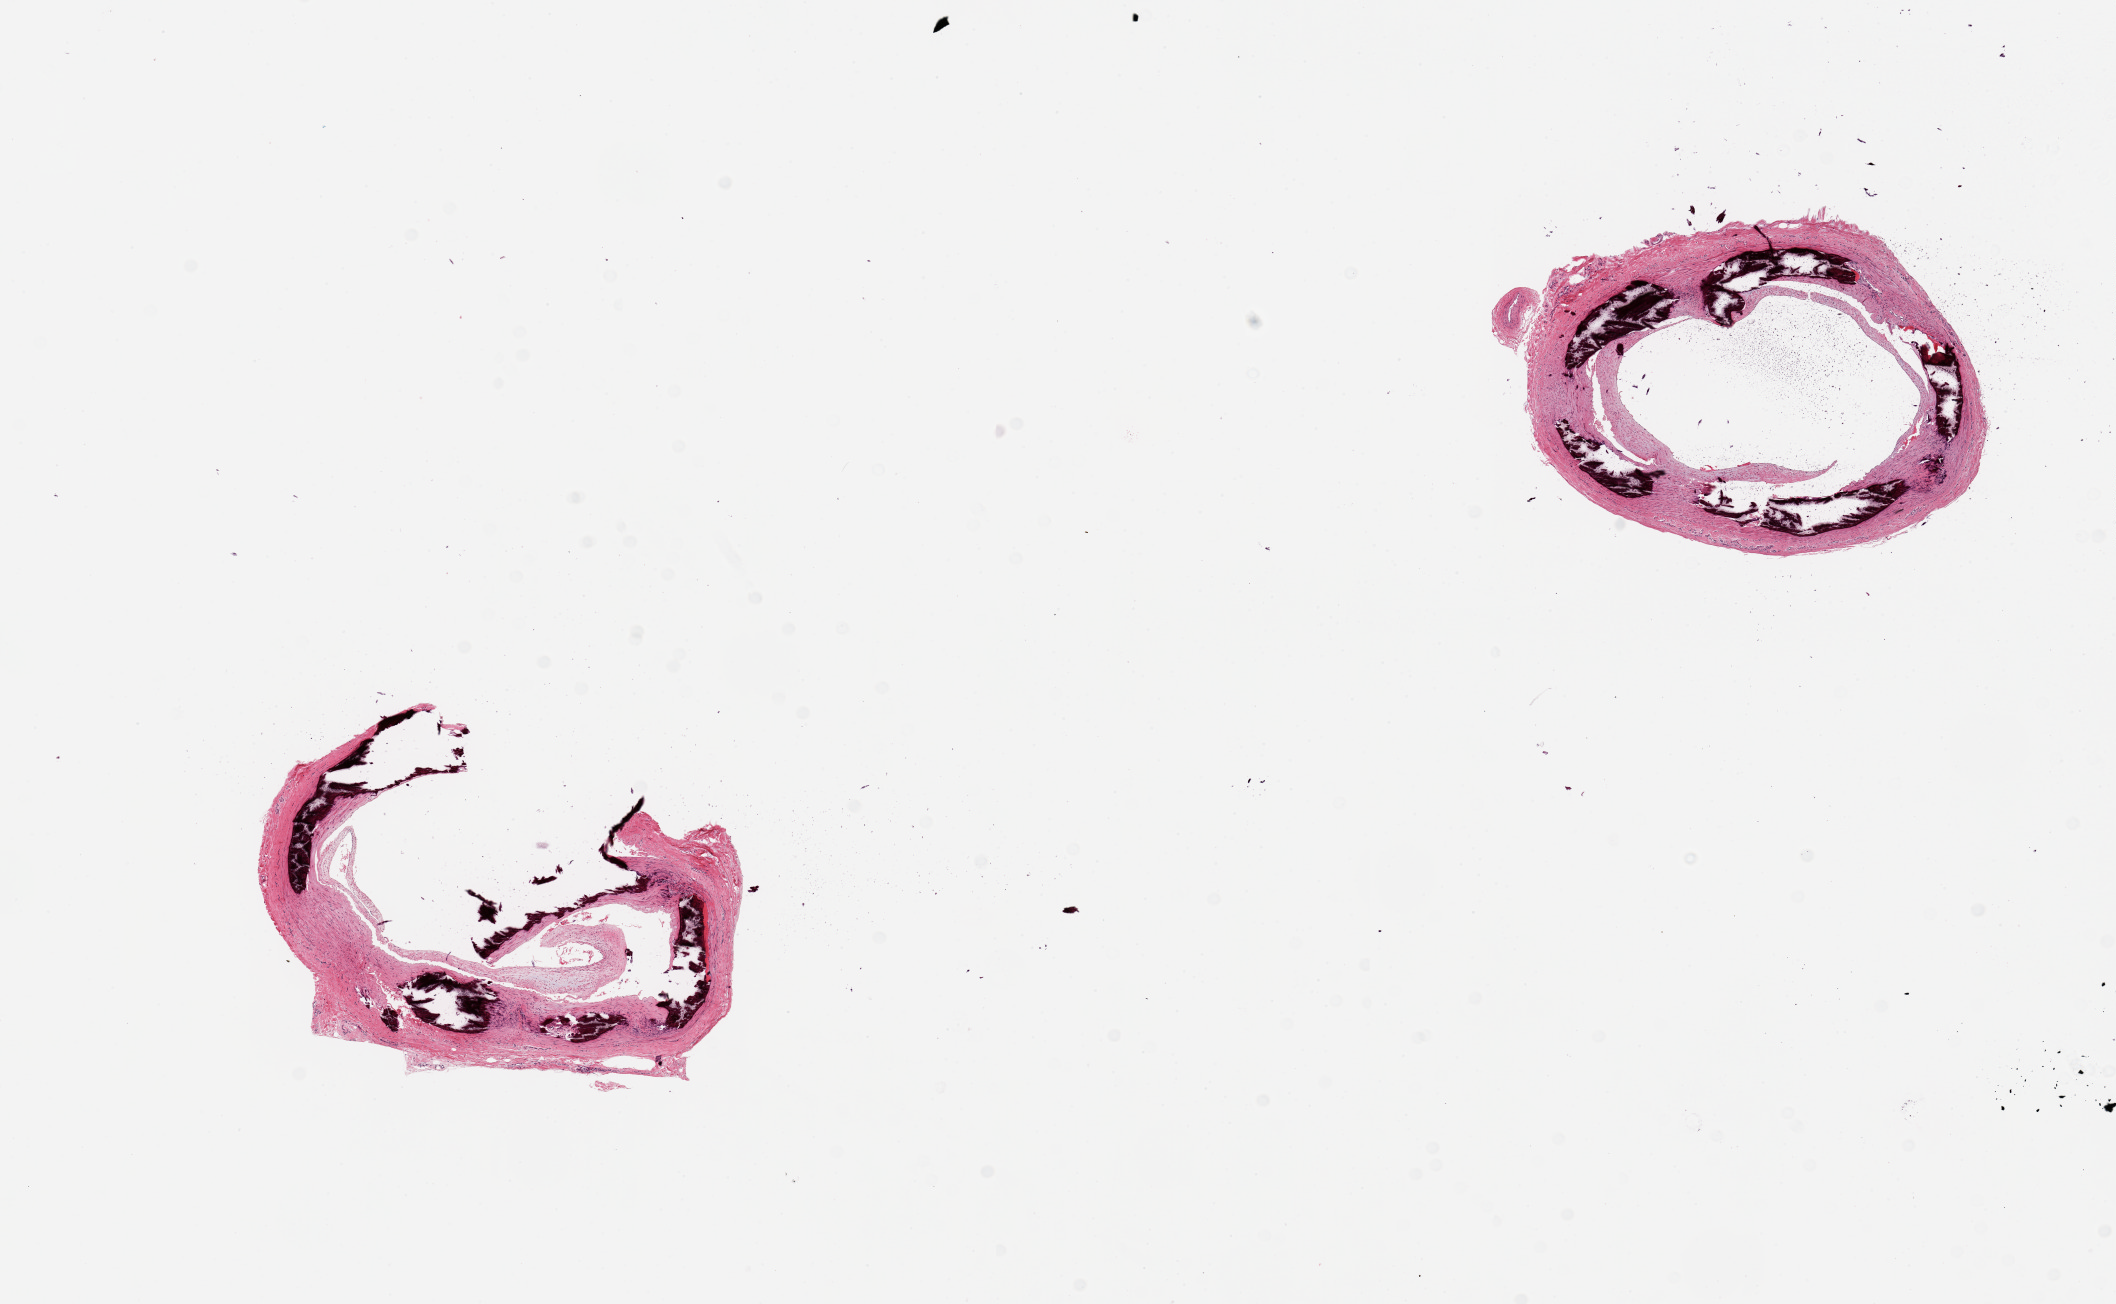
H&E whole-slide image, low-resolution overview of the scanned area, about 16.7 x 10.3 mm (acquisition: 20x scan). PAXgene-fixed, paraffin-embedded tissue. Target tissue: tibial artery. Donor tissue sample. Donor: male.
* pathologist's review note for this sample: 2 pieces; calcific atherosclerosis and some medial calcification